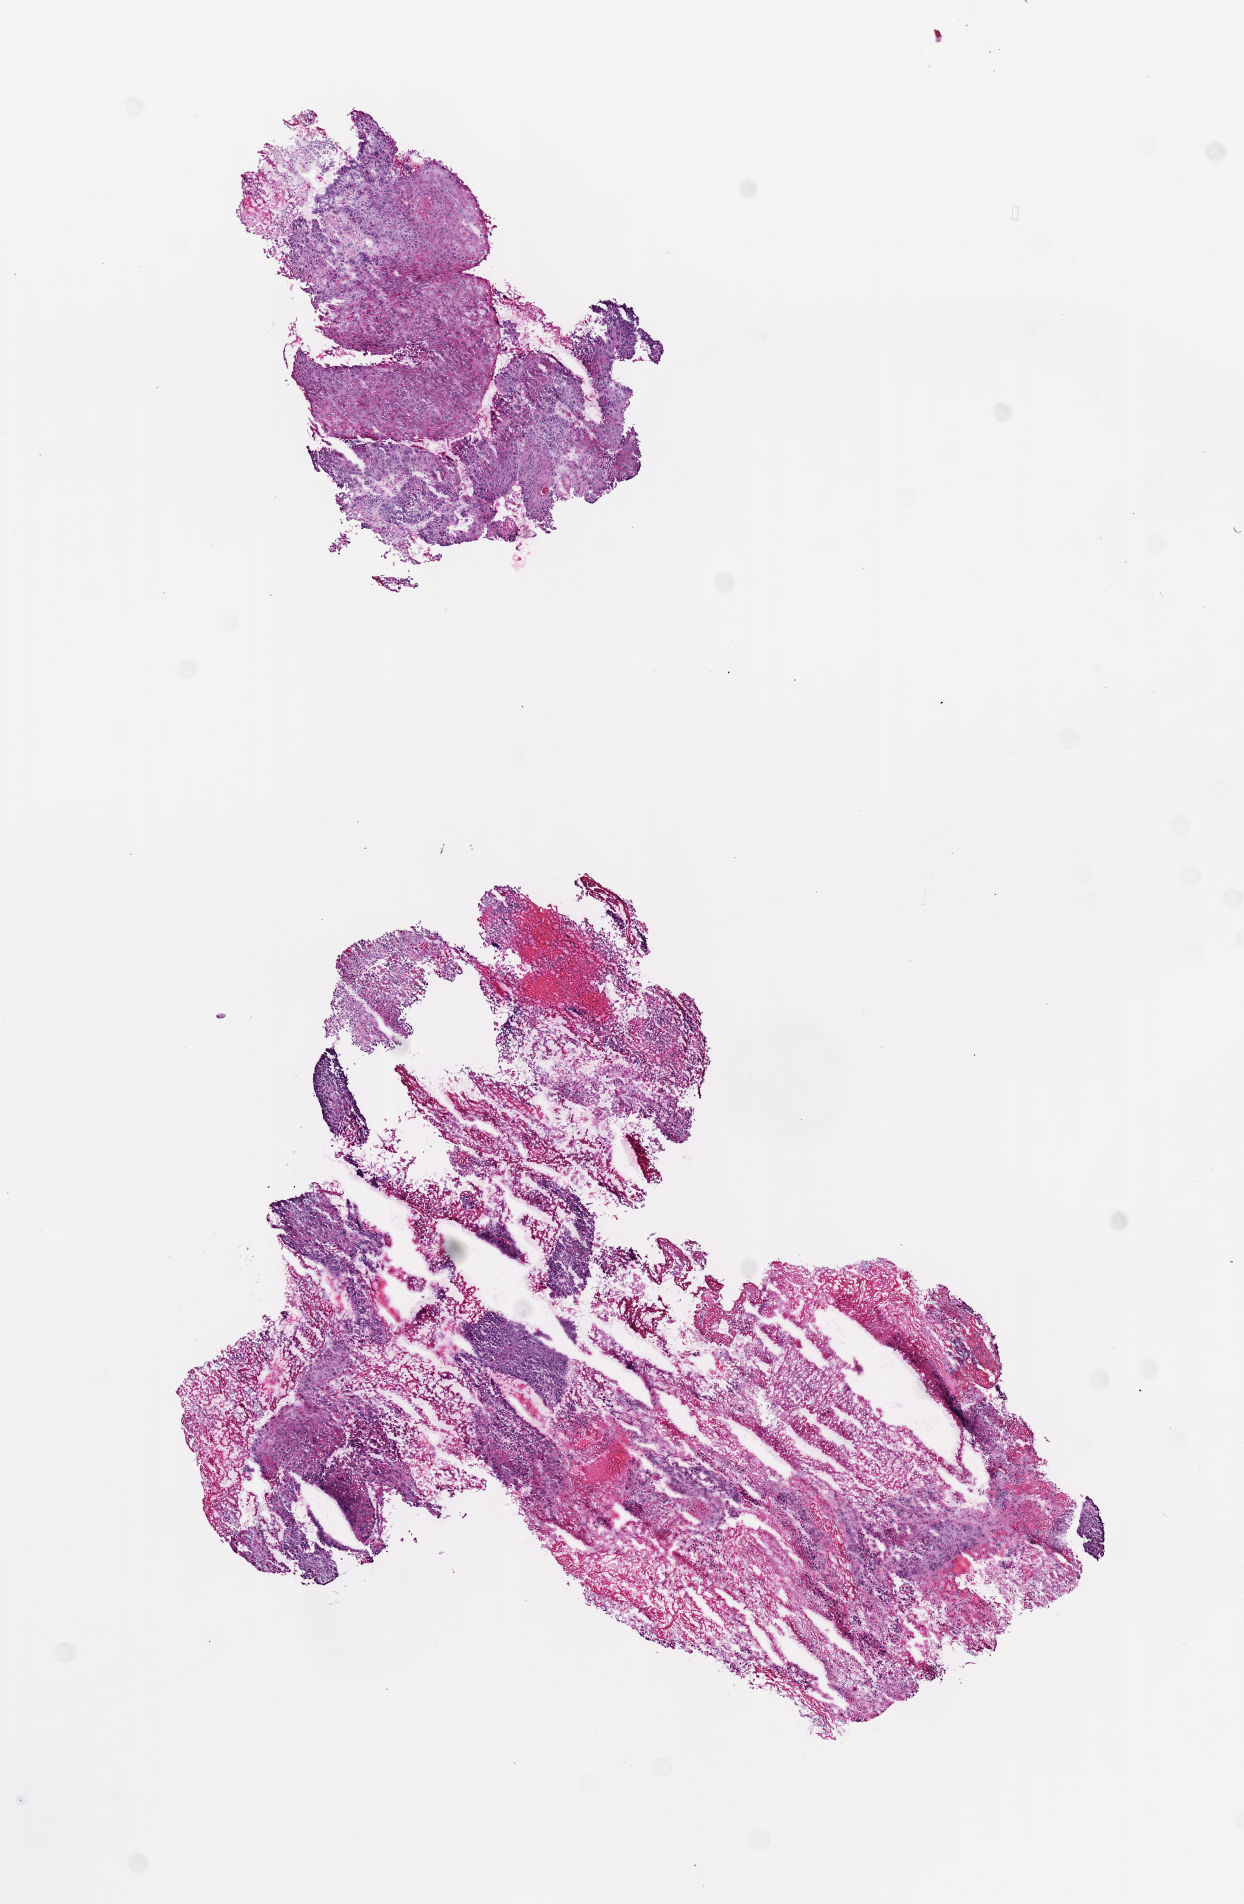
Whole-slide histology image, H&E-stained — shown as a low-resolution overview of the whole scanned area (about 5.0 x 7.7 mm, acquisition: 40x scan). Frozen section. Primary tumour sample from the esophagus. Male patient; age at initial diagnosis 55 years. Histologic grade: GX (grade cannot be assessed). Slide review estimates, as recorded: tumour cells 70%, tumour nuclei 70%, normal cells 0%, stromal cells 20%, necrosis 10%. Infiltration values recorded for this section: lymphocyte infiltration 40%, monocyte infiltration 20%, neutrophil infiltration 20%.
• histologic diagnosis: Squamous cell carcinoma, NOS (middle third of esophagus)